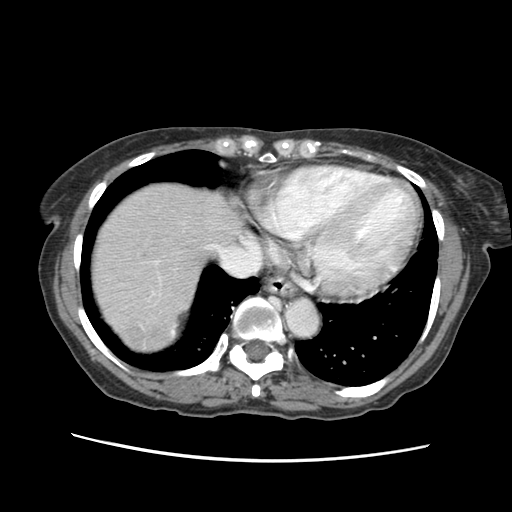
Contrast-enhanced abdominal CT (liver protocol), one axial slice; slice 53 of 63 in the series (ordered by position); reconstruction kernel STANDARD; 120 kVp; soft-tissue window (W 400 / L 40 HU); 2.5 mm slice thickness; 512 × 512 image matrix. From the clinical record (not read from this slice): diagnosis: hepatocellular carcinoma (patient treated with transarterial chemoembolisation; whether this scan precedes or follows treatment is not stated here); TNM stage (as recorded): Stage-I; Child-Pugh class: B; tumour differentiation: well differentiated; tumour nodularity: uninodular.
Structures marked on this image (semi-automatic segmentation, software-assisted and operator-edited):
- liver parenchyma outside the tumour (the mass and vessels are separate outlines, so this box may not span the whole liver): box from (x=94, y=182) to (x=240, y=348) px
- mass: (x=120, y=311)–(x=170, y=346)
- liver vessels: (x=171, y=329)–(x=174, y=333)